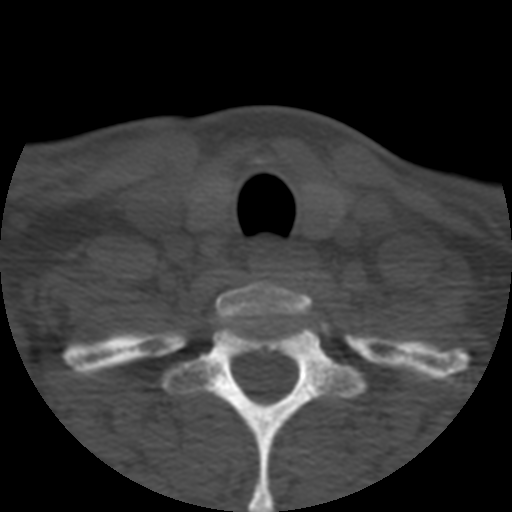
CT including the spine, one axial slice. Slice 452 of 508 in the series (ordered by position). Reconstruction kernel STANDARD. 120 kVp. Bone window (W 1800 / L 400 HU). 512 × 512 image matrix, field of view 160 × 160 mm. Patient age 57 years. From the clinical record (not read from this slice): primary cancer: prostate.
Annotated regions visible in this slice (semi-automatic segmentation, software-assisted and operator-edited):
- T1 vertebra: bounding box [x1, y1, x2, y2] px = [78, 309, 415, 512]